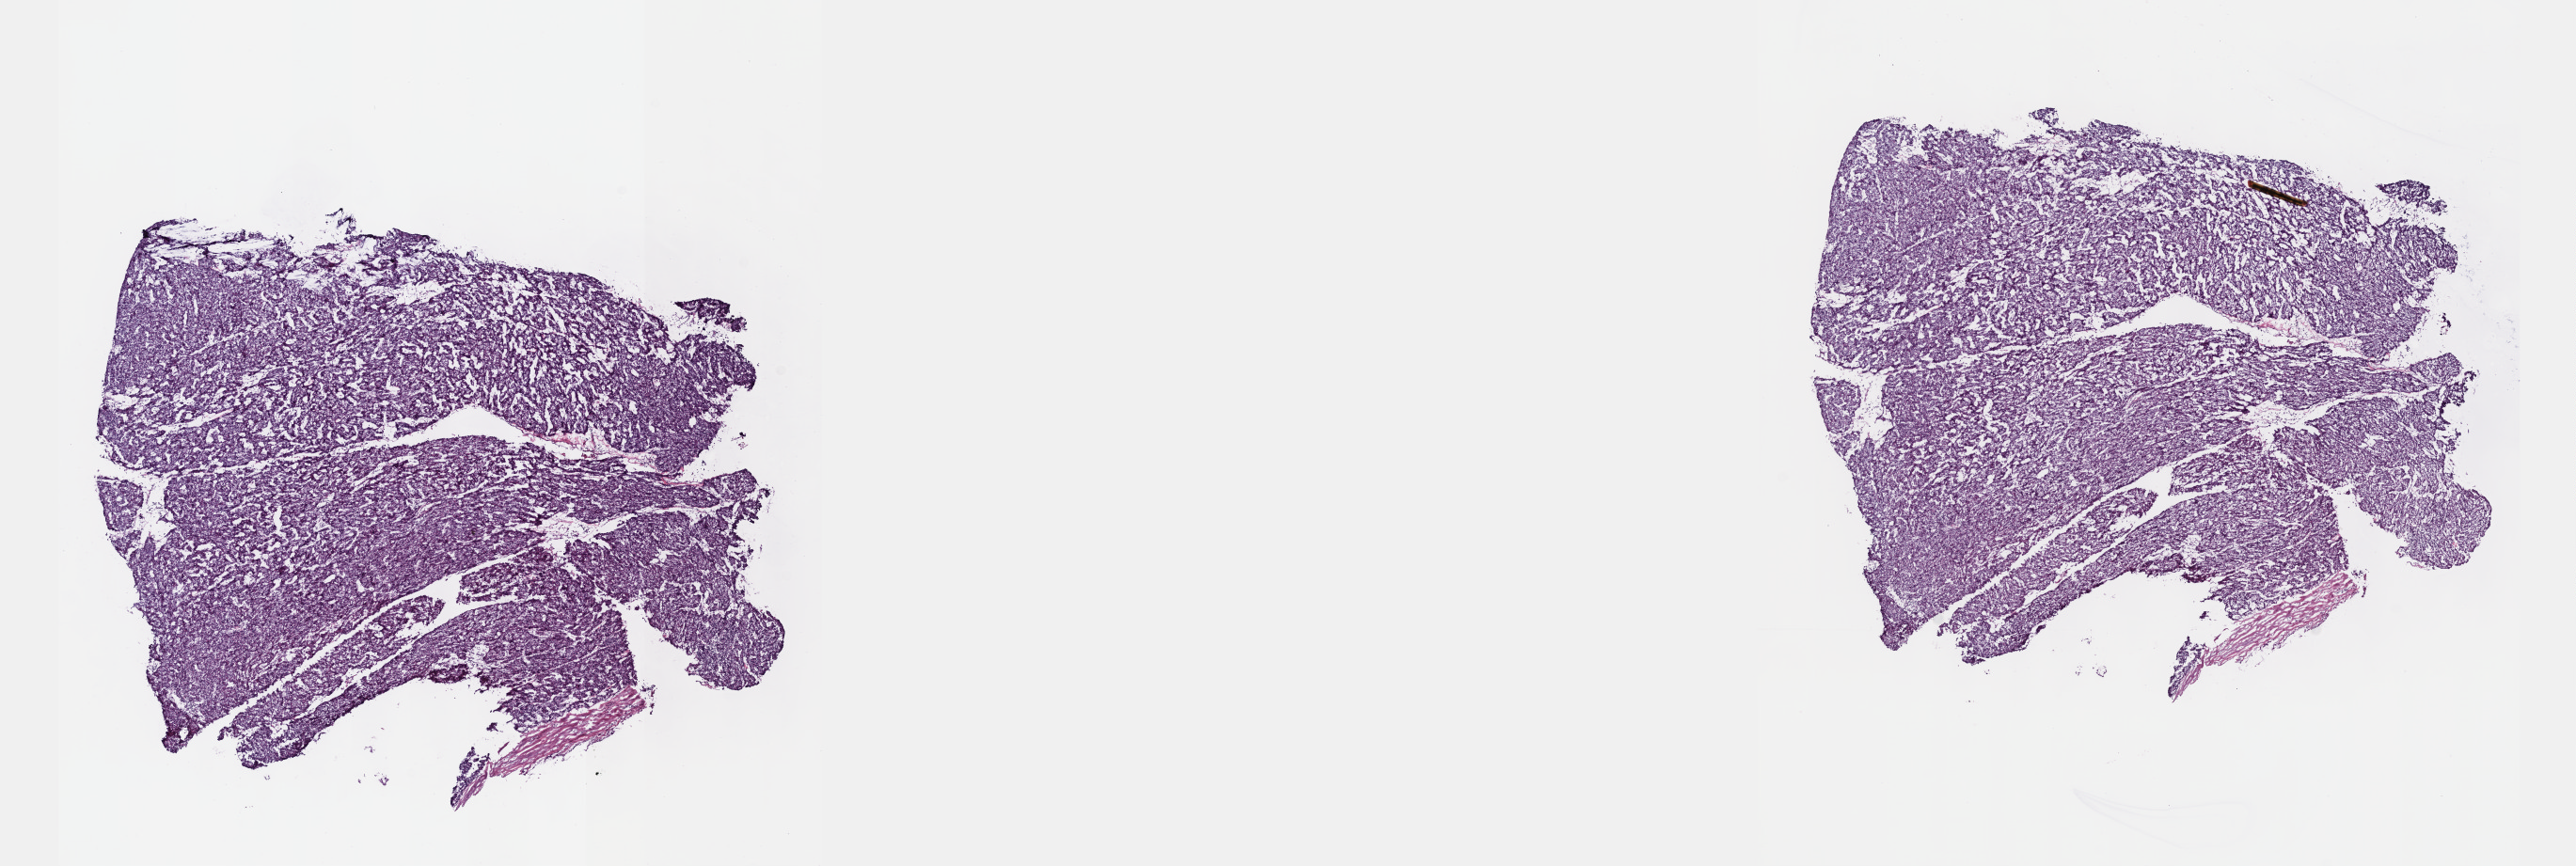
Whole-slide histology image, H&E, shown as a low-resolution overview of the whole scanned area (about 22.1 x 7.4 mm, acquisition: 40x scan); frozen section from the top of the tissue portion; primary tumour sample from the thymus. Patient: female, age at initial diagnosis 76 years. Slide review estimates, as recorded: tumour cells 92%, tumour nuclei 70%, normal cells 0%, stromal cells 8%, necrosis 0%. Inflammatory infiltration, as recorded: lymphocyte infiltration 25%, monocyte infiltration 0%, neutrophil infiltration 0%.
Pathologic diagnosis: Thymoma, type A, malignant.